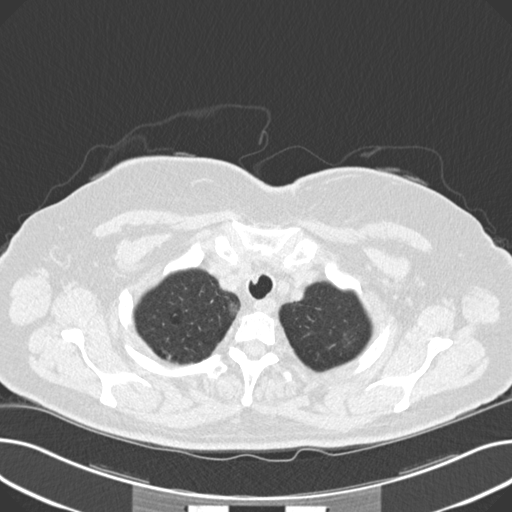
Chest CT (low-dose screening protocol), one axial image; third annual screen; lung window (W 1500 / L -600 HU); standard (soft-tissue) reconstruction kernel (B30f); 512 × 512 image matrix. Female, age 60 years at enrolment. Current smoker at enrolment.
• Expert-annotated lung lesion, bounding box <326,326,373,360> (left, top, right, bottom; pixels).
• The screening reader recorded 8 non-calcified nodules or masses ≥4 mm on this exam (right upper lobe, lingula, lingula, right middle lobe, right lower lobe, left lower lobe, left lower lobe, left lower lobe); which of them this box marks is not recorded.
• Official screen result: positive, other.
• Lung cancer was diagnosed 176 days after this screen: non-small cell carcinoma, left upper lobe, poorly differentiated (G3), stage IB (AJCC 6th edition), 7 mm at pathology.